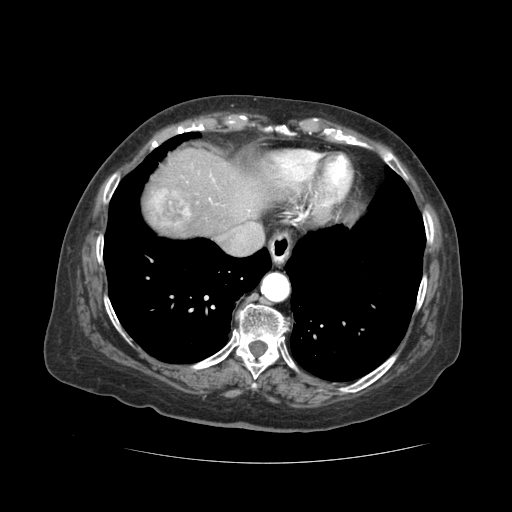
Contrast-enhanced abdominal CT (liver protocol), one axial slice. Slice 44 of 59 in the series (ordered by position). 120 kVp. Soft-tissue window (W 400 / L 40 HU). 512 × 512 image matrix, field of view 380 × 380 mm. From the clinical record (not read from this slice): diagnosis: hepatocellular carcinoma (patient treated with transarterial chemoembolisation; whether this scan precedes or follows treatment is not stated here); TNM stage (as recorded): Stage-I.
Annotated regions visible in this slice (semi-automatic segmentation, software-assisted and operator-edited):
- liver parenchyma outside the tumour (the mass and vessels are separate outlines, so this box may not span the whole liver): bounding box <144,148,268,236> (left, top, right, bottom; pixels)
- mass: <151,189,190,229>
- liver vessels: <209,175,250,212>